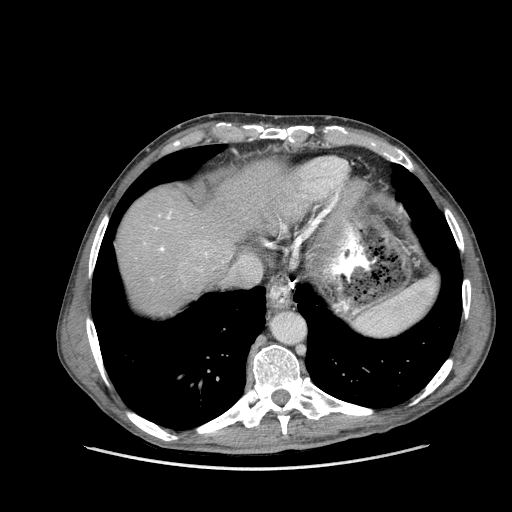
Contrast-enhanced abdominal CT (liver protocol), one axial slice. Position 133 of 162 along the scan axis. Reconstruction kernel STANDARD. 100 kVp. Soft-tissue window (W 400 / L 40 HU). 2.5 mm slice thickness. 512 × 512 image matrix. From the clinical record (not read from this slice): diagnosis: hepatocellular carcinoma (patient treated with transarterial chemoembolisation; whether this scan precedes or follows treatment is not stated here); TNM stage (as recorded): Stage-IIIA; Child-Pugh class: A; tumour nodularity: multinodular; tumour size: 9.9 cm.
Structures marked on this image (semi-automatic segmentation, software-assisted and operator-edited):
- abdominal aorta: bounding box [x1, y1, x2, y2] px = [273, 313, 304, 344]
- liver parenchyma outside the tumour (the mass and vessels are separate outlines, so this box may not span the whole liver): [116, 162, 282, 314]
- liver vessels: [155, 211, 207, 255]